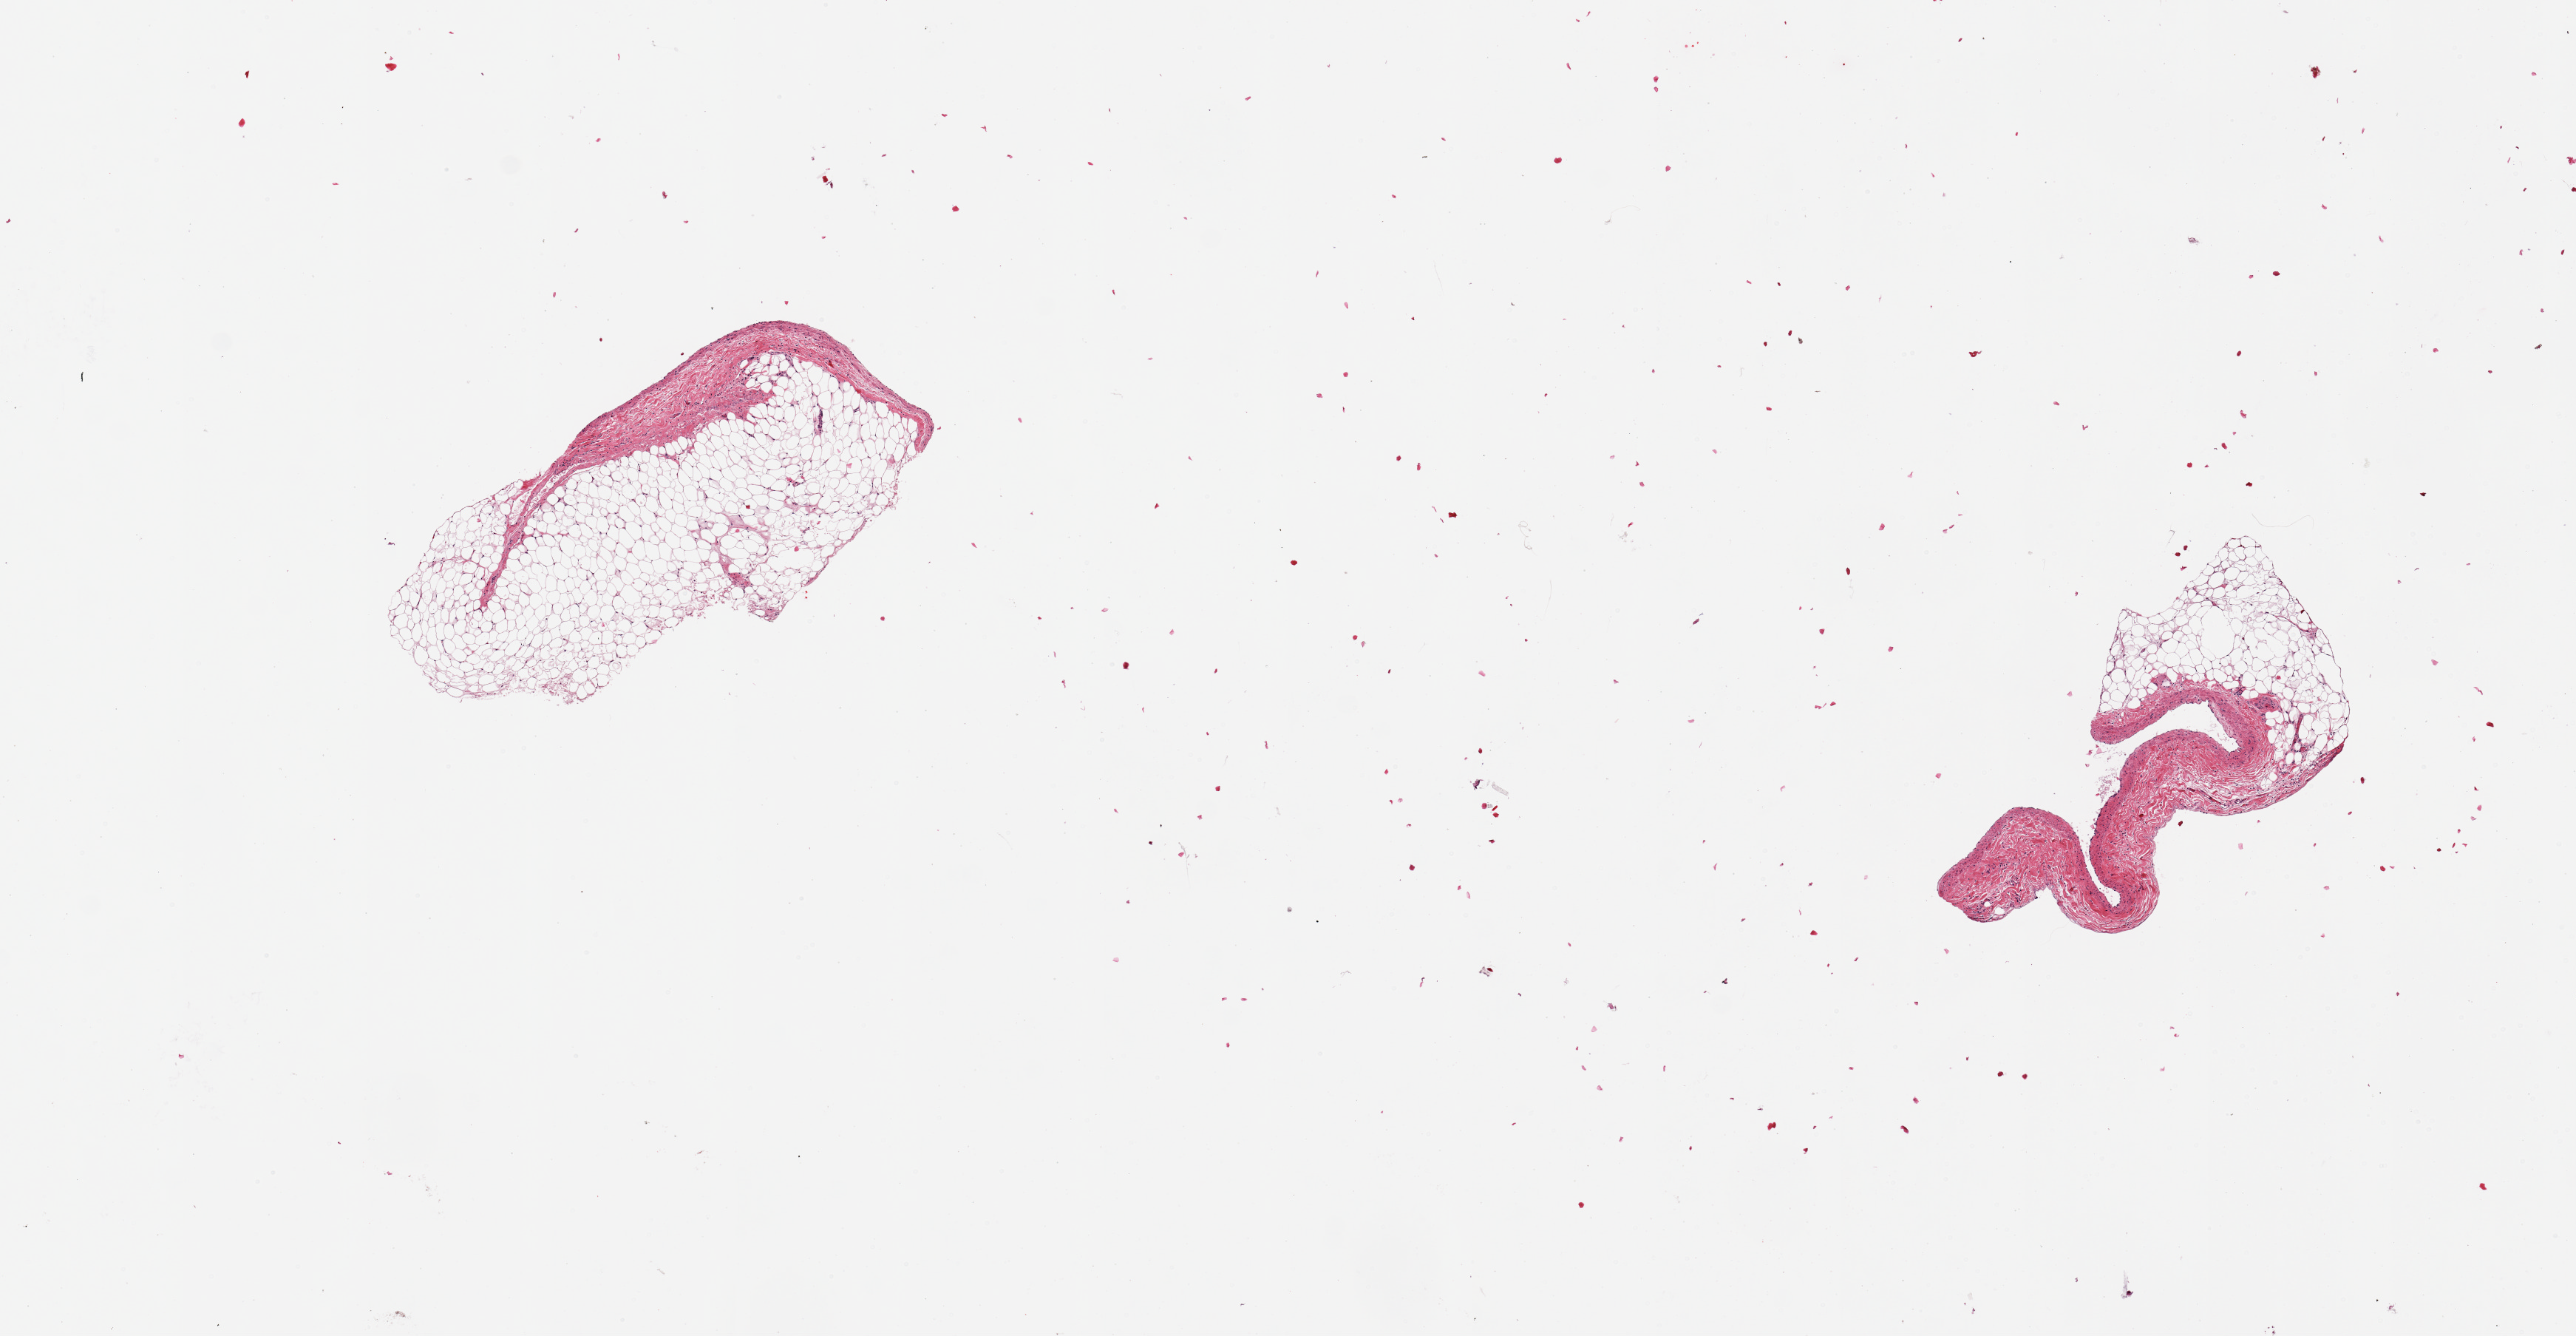
Hematoxylin and eosin (H&E) whole-slide image, brightfield, a low-resolution overview of the entire scanned area, about 13.8 x 7.1 mm (slide scanned at 20x); PAXgene-fixed, paraffin-embedded tissue; sampled site (target tissue): coronary artery; tissue donor sample. Donor: male.
* reviewer comment on this tissue sample: 2 pieces, one piece is 90% fat with strip of vessel, second is 40% fat